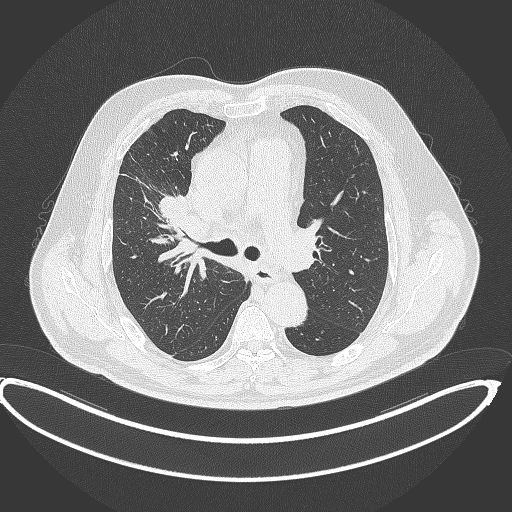
Chest CT, one axial slice; position 261 of 390 along the scan axis; reconstruction kernel B70f; 120 kVp; lung window (W 1500 / L -600 HU); 1 mm slice thickness; 512 × 512 image matrix. Male patient, age 62 years. From the clinical record (not read from this slice): clinical TNM (as recorded): T1c N3 M1c.
Outlined on this slice (rectangle marked by the reading radiologist):
- lung tumour (recorded histology: adenocarcinoma): bounding box <157,194,192,233> (left, top, right, bottom; pixels)